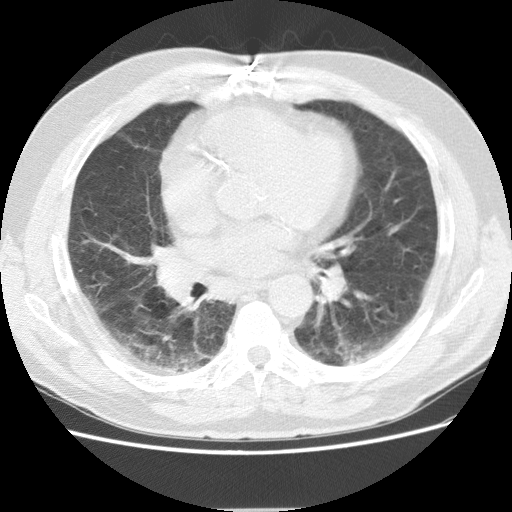
Low-dose screening chest CT, axial slice; baseline annual screen; lung window (W 1500 / L -600 HU); 2.5 mm slice thickness; slice 68 of 155 in the series. Male participant, aged 72 years at enrolment. Former smoker at enrolment.
Expert-annotated lung lesion, bounding box [x1, y1, x2, y2] px = [147, 236, 195, 273]. Screening reader's record for this exam: no non-calcified nodule ≥4 mm recorded. Participant outcome: lung cancer diagnosed 163 days after this screen — adenocarcinoma, NOS, right middle lobe, stage IIIB (AJCC 6th edition), 27 mm at pathology.